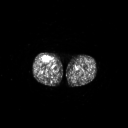
FDG PET of an extremity soft-tissue mass (from a PET/CT study), one axial slice; position 257 of 311 along the scan axis; 3.27 mm slice thickness; 128 × 128 image matrix, field of view 700 × 700 mm. Male patient, age 56 years. From the clinical record (not read from this slice): histological type: pleiomorphic leiomyosarcoma; grade: intermediate; site of the primary tumour: right thigh.
Annotated regions visible in this slice (expert contour drawn on MRI and transferred to this co-registered scan by the dataset authors):
- gross tumour volume including surrounding oedema: bounding box (x1, y1, x2, y2) in pixels: (42, 56, 51, 62)